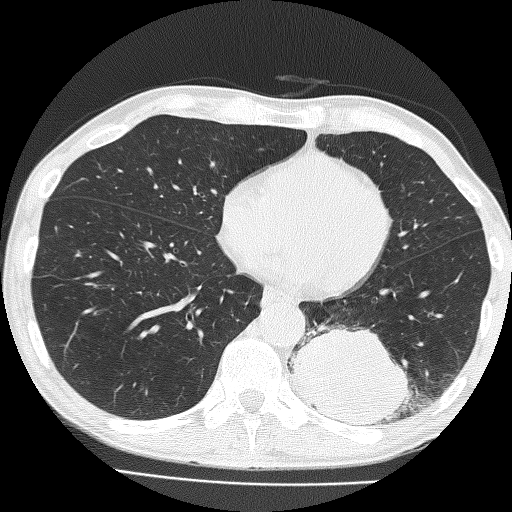
Low-dose screening chest CT, one axial slice. Position 62 of 160 along the scan axis. 120 kVp. Lung window (W 1500 / L -600 HU). 2 mm slice thickness. 512 × 512 image matrix, field of view 324 × 324 mm.
Outlined on this slice (expert manual segmentation):
- lesion 1 (tumor, lower lobe of left lung): bounding box (x1, y1, x2, y2) in pixels: (292, 326, 410, 425)